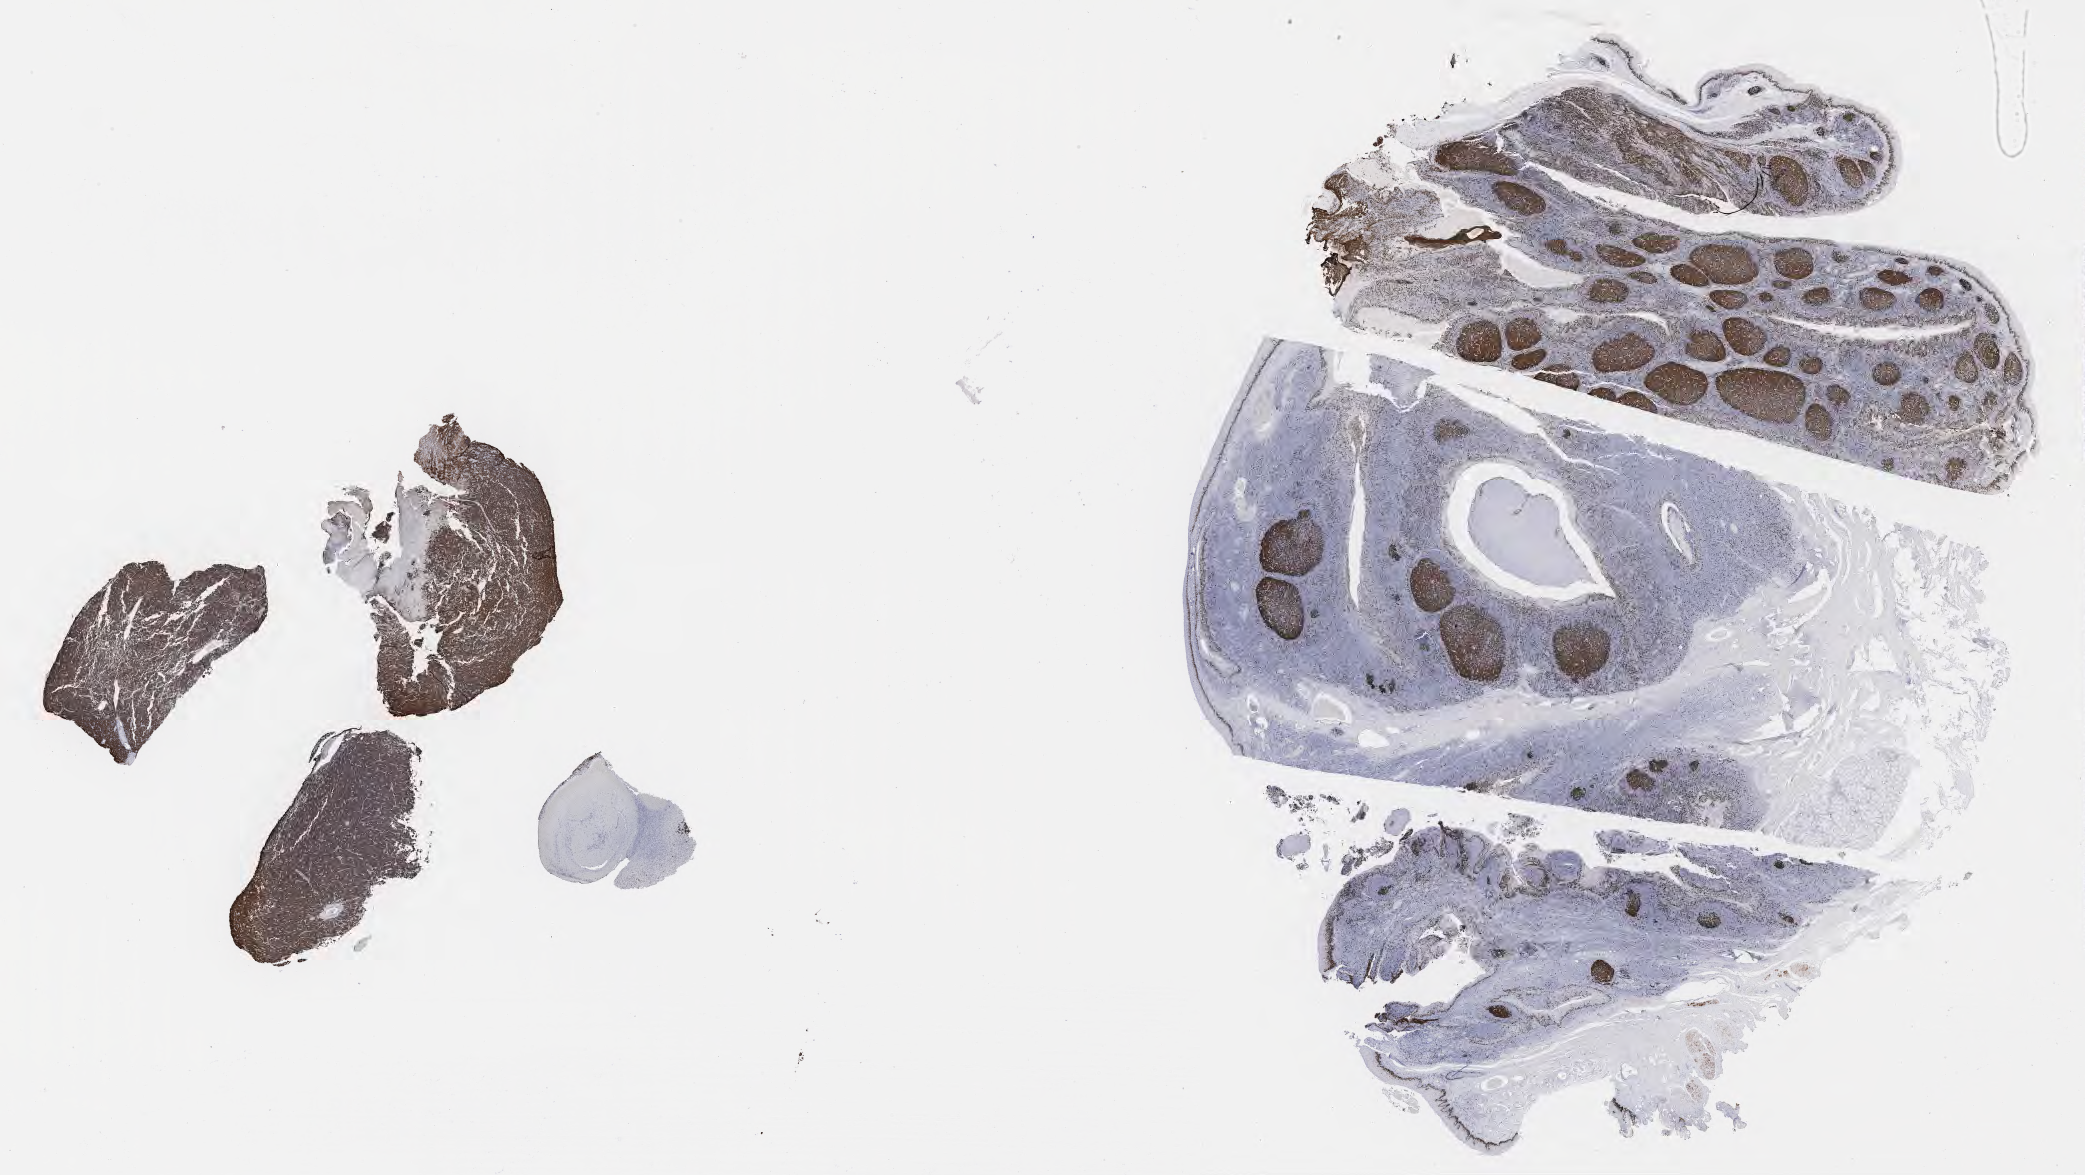
IHC for Ki-67, whole-slide image, whole scanned area (about 33.7 x 19.0 mm) shown as a low-resolution overview, specimen: tumor tissue. Male patient, aged 10.
• diagnosis: Burkitt lymphoma, NOS